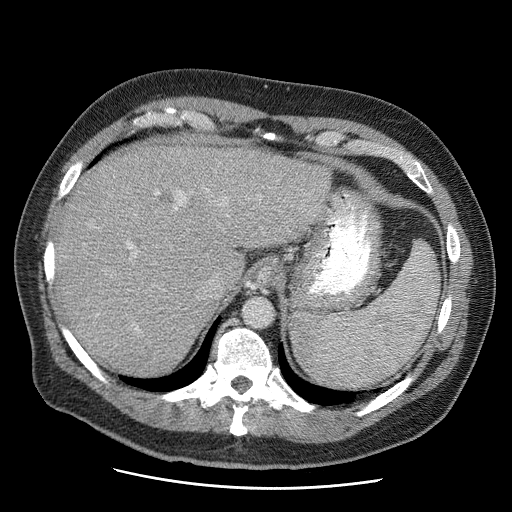
Contrast-enhanced abdominal CT (liver protocol), one axial slice; reconstruction kernel STANDARD; soft-tissue window (W 400 / L 40 HU); 2.5 mm slice thickness; 512 × 512 image matrix, field of view 380 × 380 mm. From the clinical record (not read from this slice): diagnosis: hepatocellular carcinoma (patient treated with transarterial chemoembolisation; whether this scan precedes or follows treatment is not stated here); TNM stage (as recorded): Stage-IIIA; Child-Pugh class: A; tumour differentiation: moderately differentiated; tumour nodularity: multinodular.
Outlined on this slice (semi-automatically segmented with operator editing):
- liver parenchyma outside the tumour (the mass and vessels are separate outlines, so this box may not span the whole liver): bounding box [x1, y1, x2, y2] px = [55, 142, 328, 374]
- liver vessels: [127, 189, 209, 330]